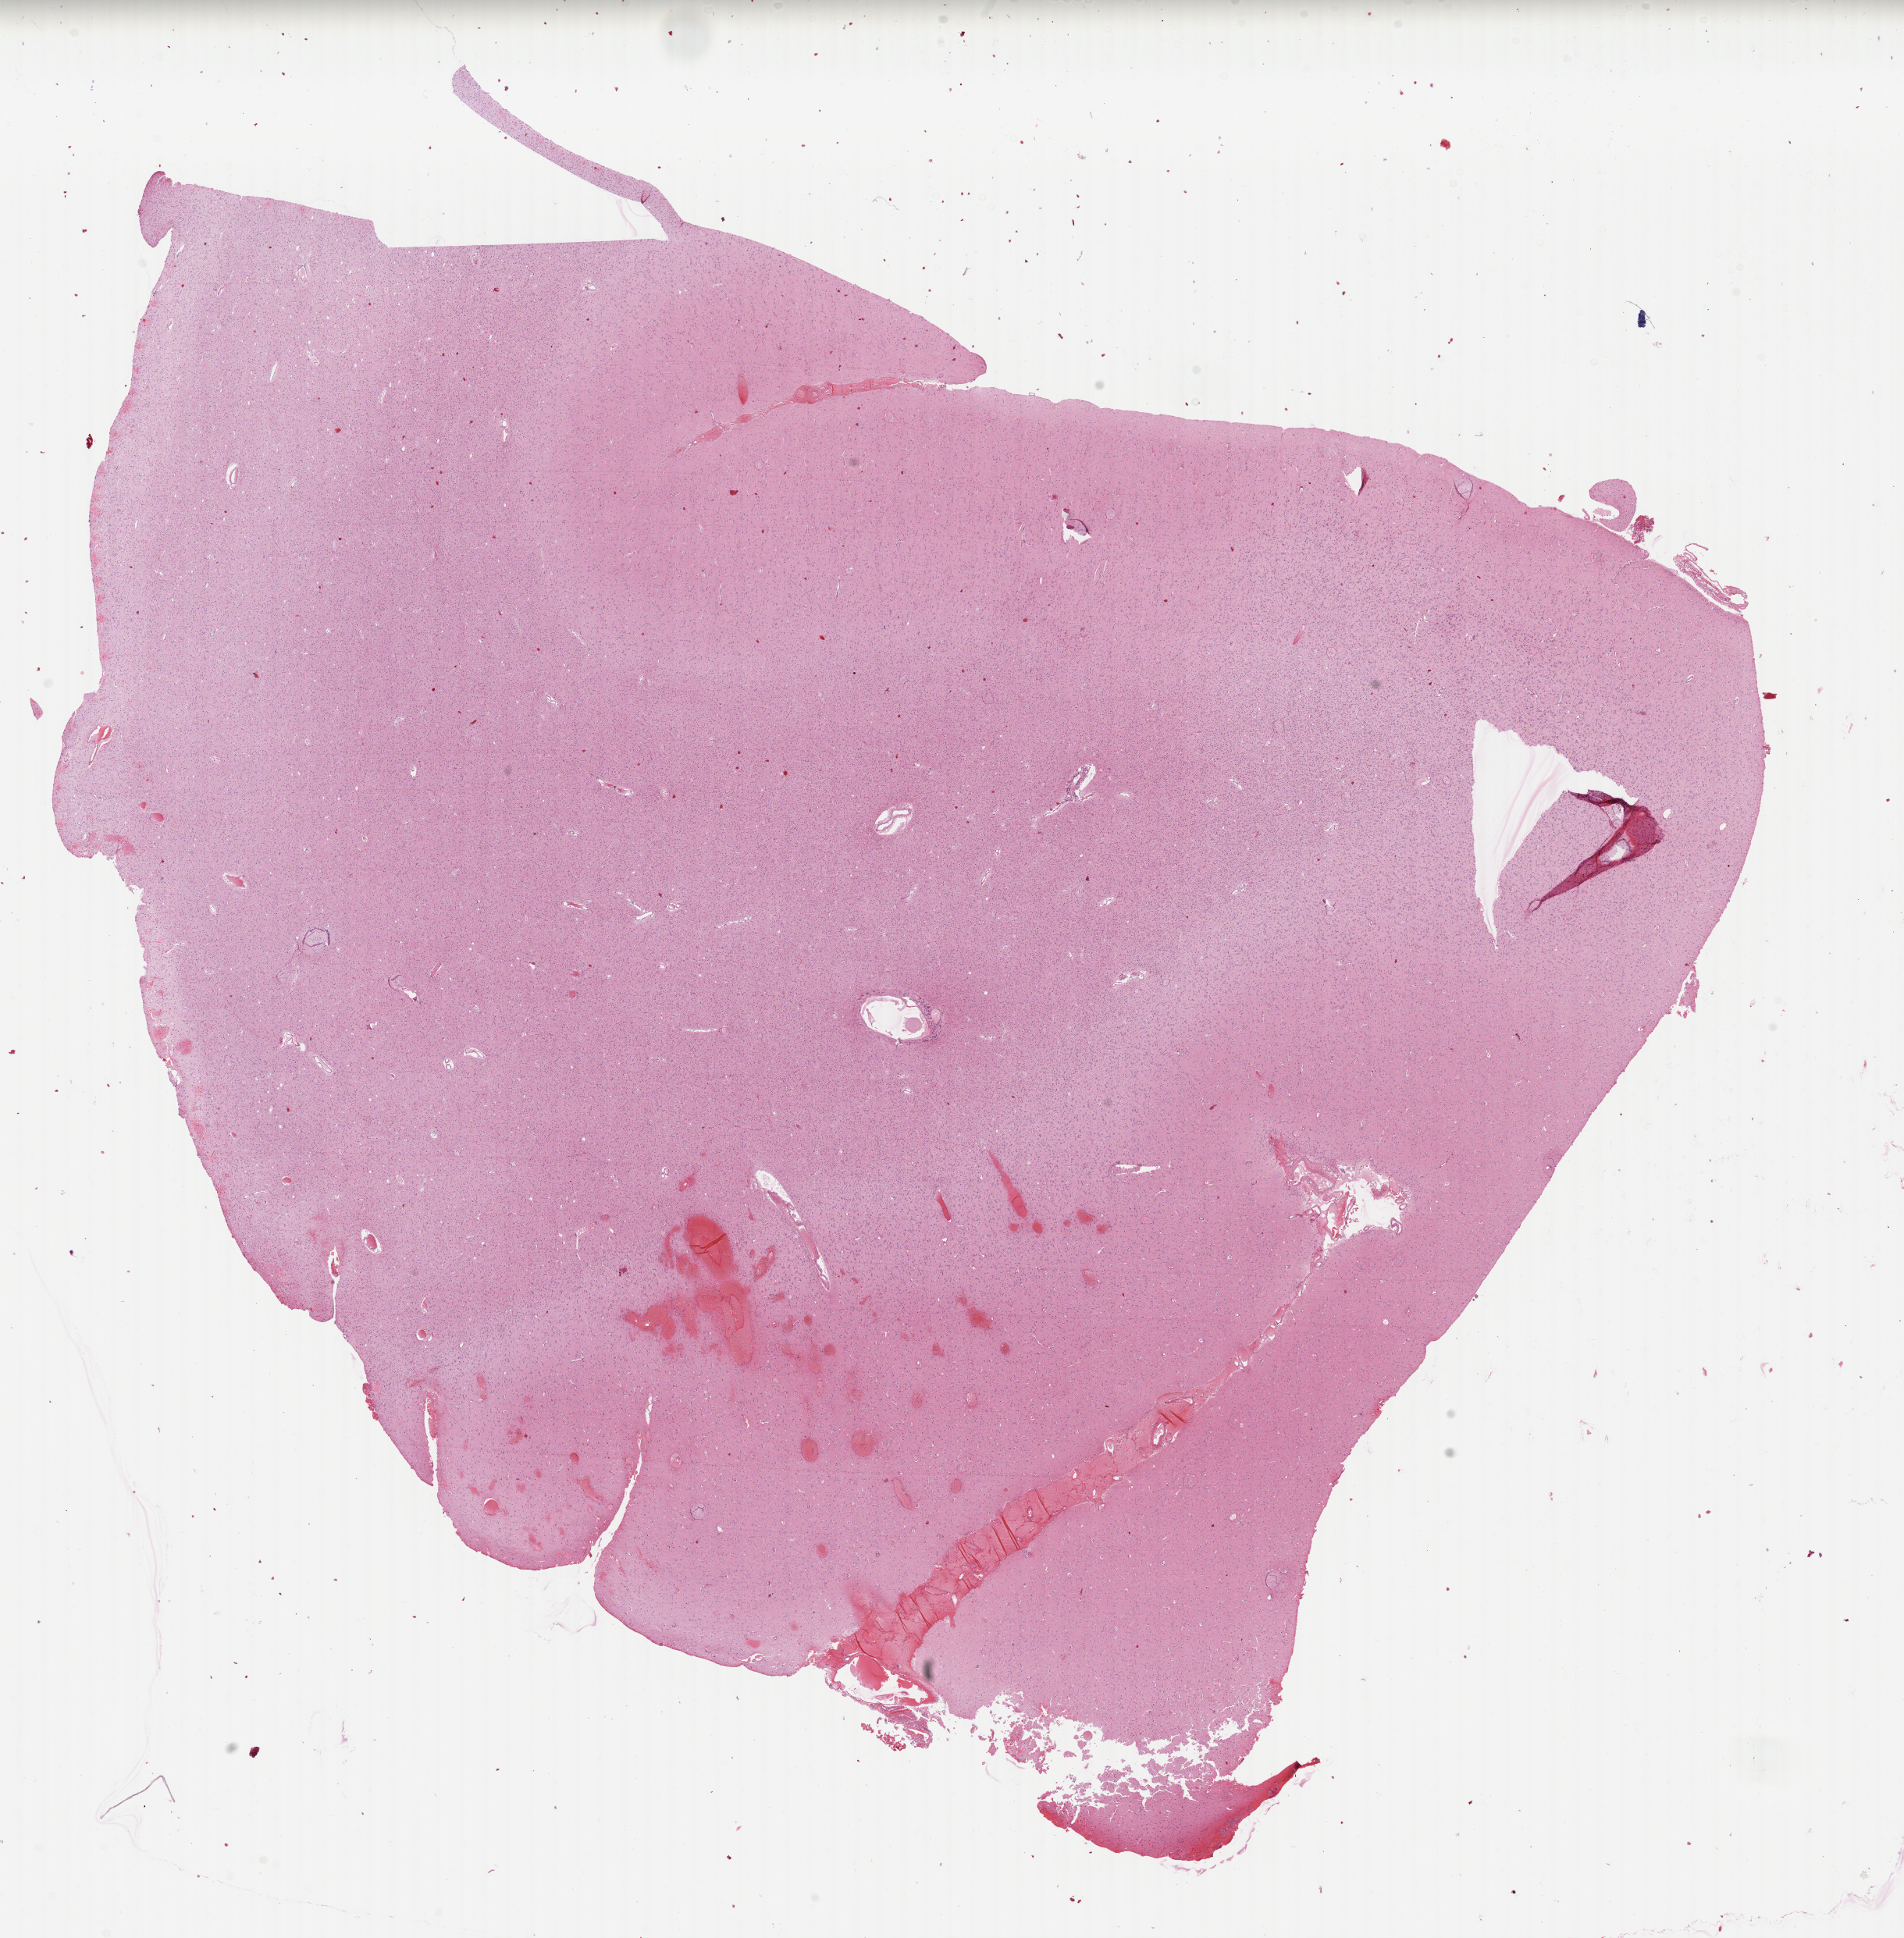
Whole-slide histology image, H&E, a low-resolution overview of the entire scanned area, about 19.2 x 19.6 mm (from a 40x scan), FFPE section, brain, primary tumour sample. Male, age 38 years at initial diagnosis. Histologic grade: G2 (moderately differentiated).
Histologic diagnosis: Mixed glioma (cerebrum). Laterality: right.